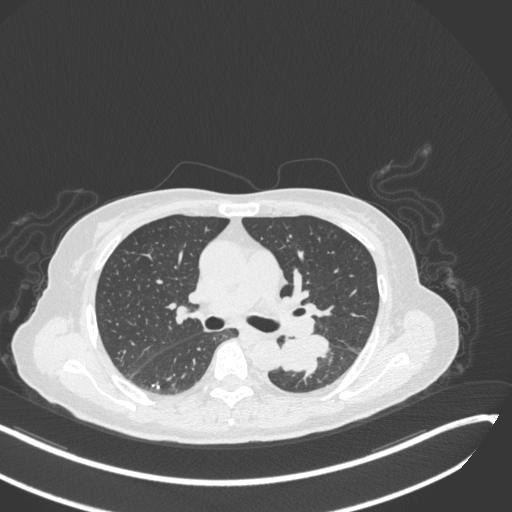
Chest CT, one axial slice. Position 169 of 342 along the scan axis. Lung window (W 1500 / L -600 HU). 1 mm slice thickness. 512 × 512 image matrix, field of view 400 × 400 mm. Patient: female, 64 years. From the clinical record (not read from this slice): clinical TNM (as recorded): T3 N1 M1.
Structures marked on this image (rectangle marked by the reading radiologist):
- lung tumour (recorded histology: small cell carcinoma): bounding box (x1, y1, x2, y2) in pixels: (278, 329, 330, 377)